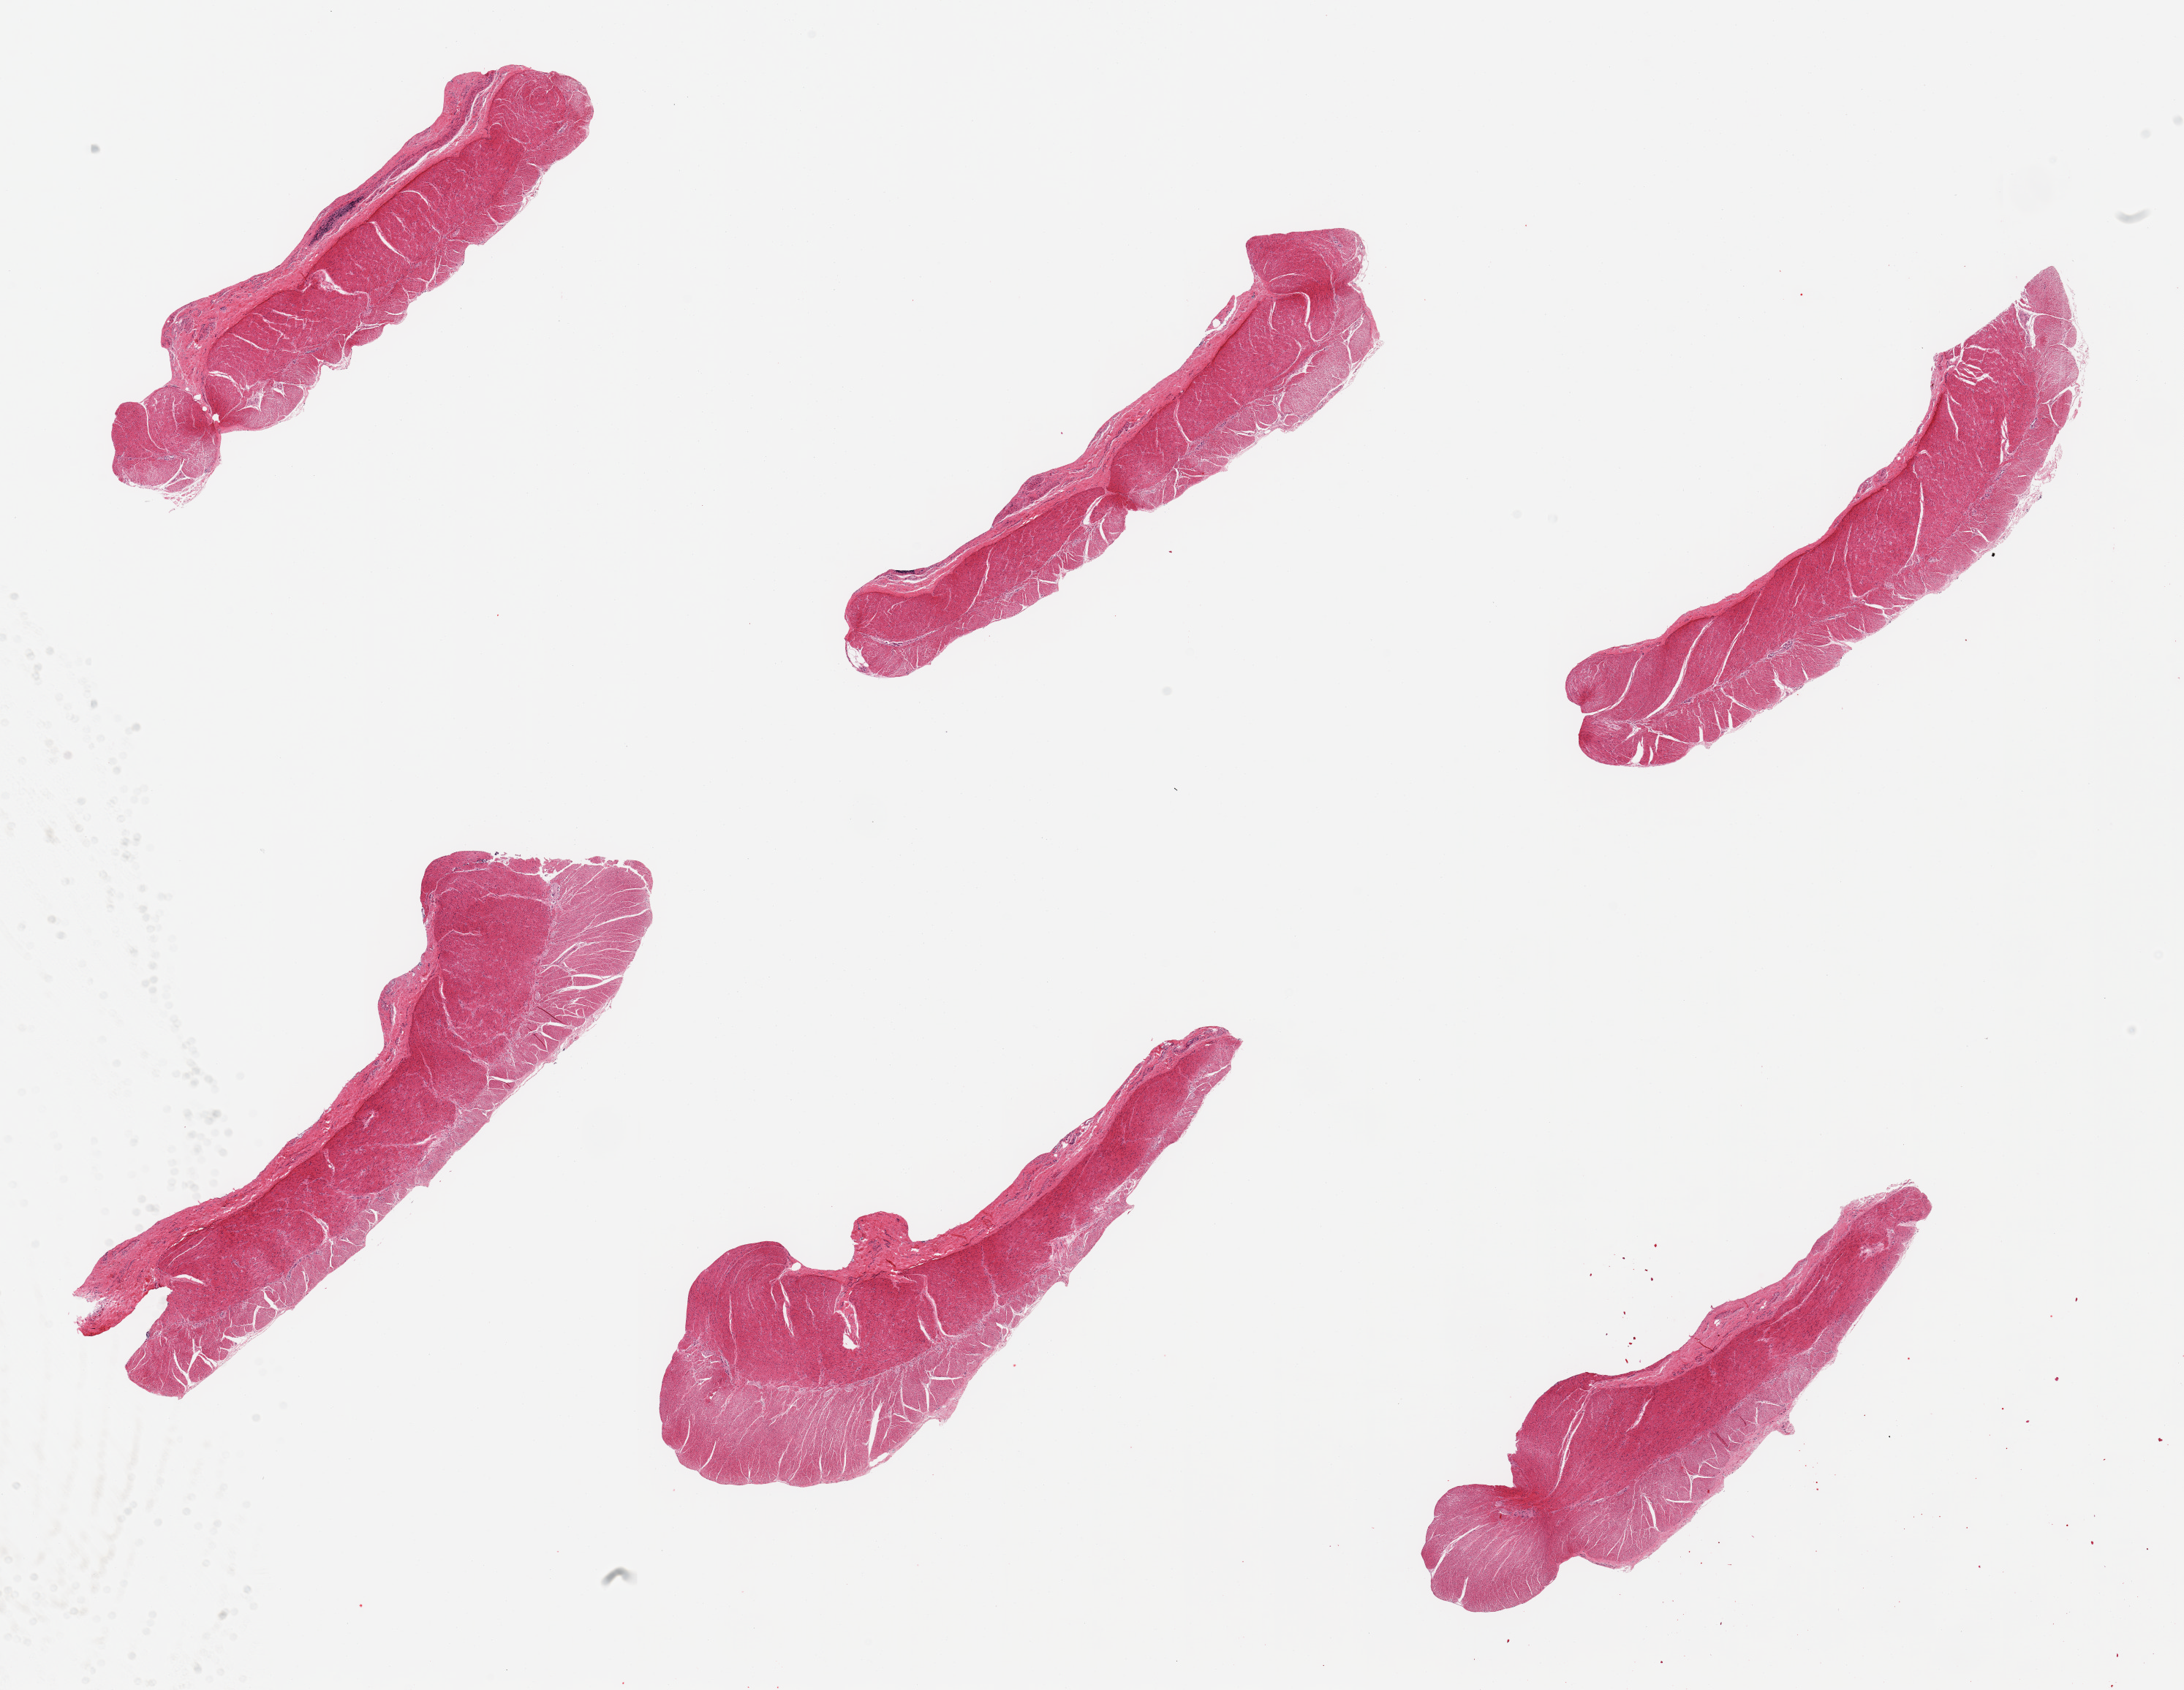
Digitized H&E-stained section, brightfield, low-resolution overview of the scanned area, about 23.6 x 18.3 mm (slide scanned at 20x), PAXgene-fixed, paraffin-embedded tissue, target tissue: sigmoid colon, donor tissue sample. Donor: male.
Pathologist's review note for this sample: 6 pieces; well dissected.